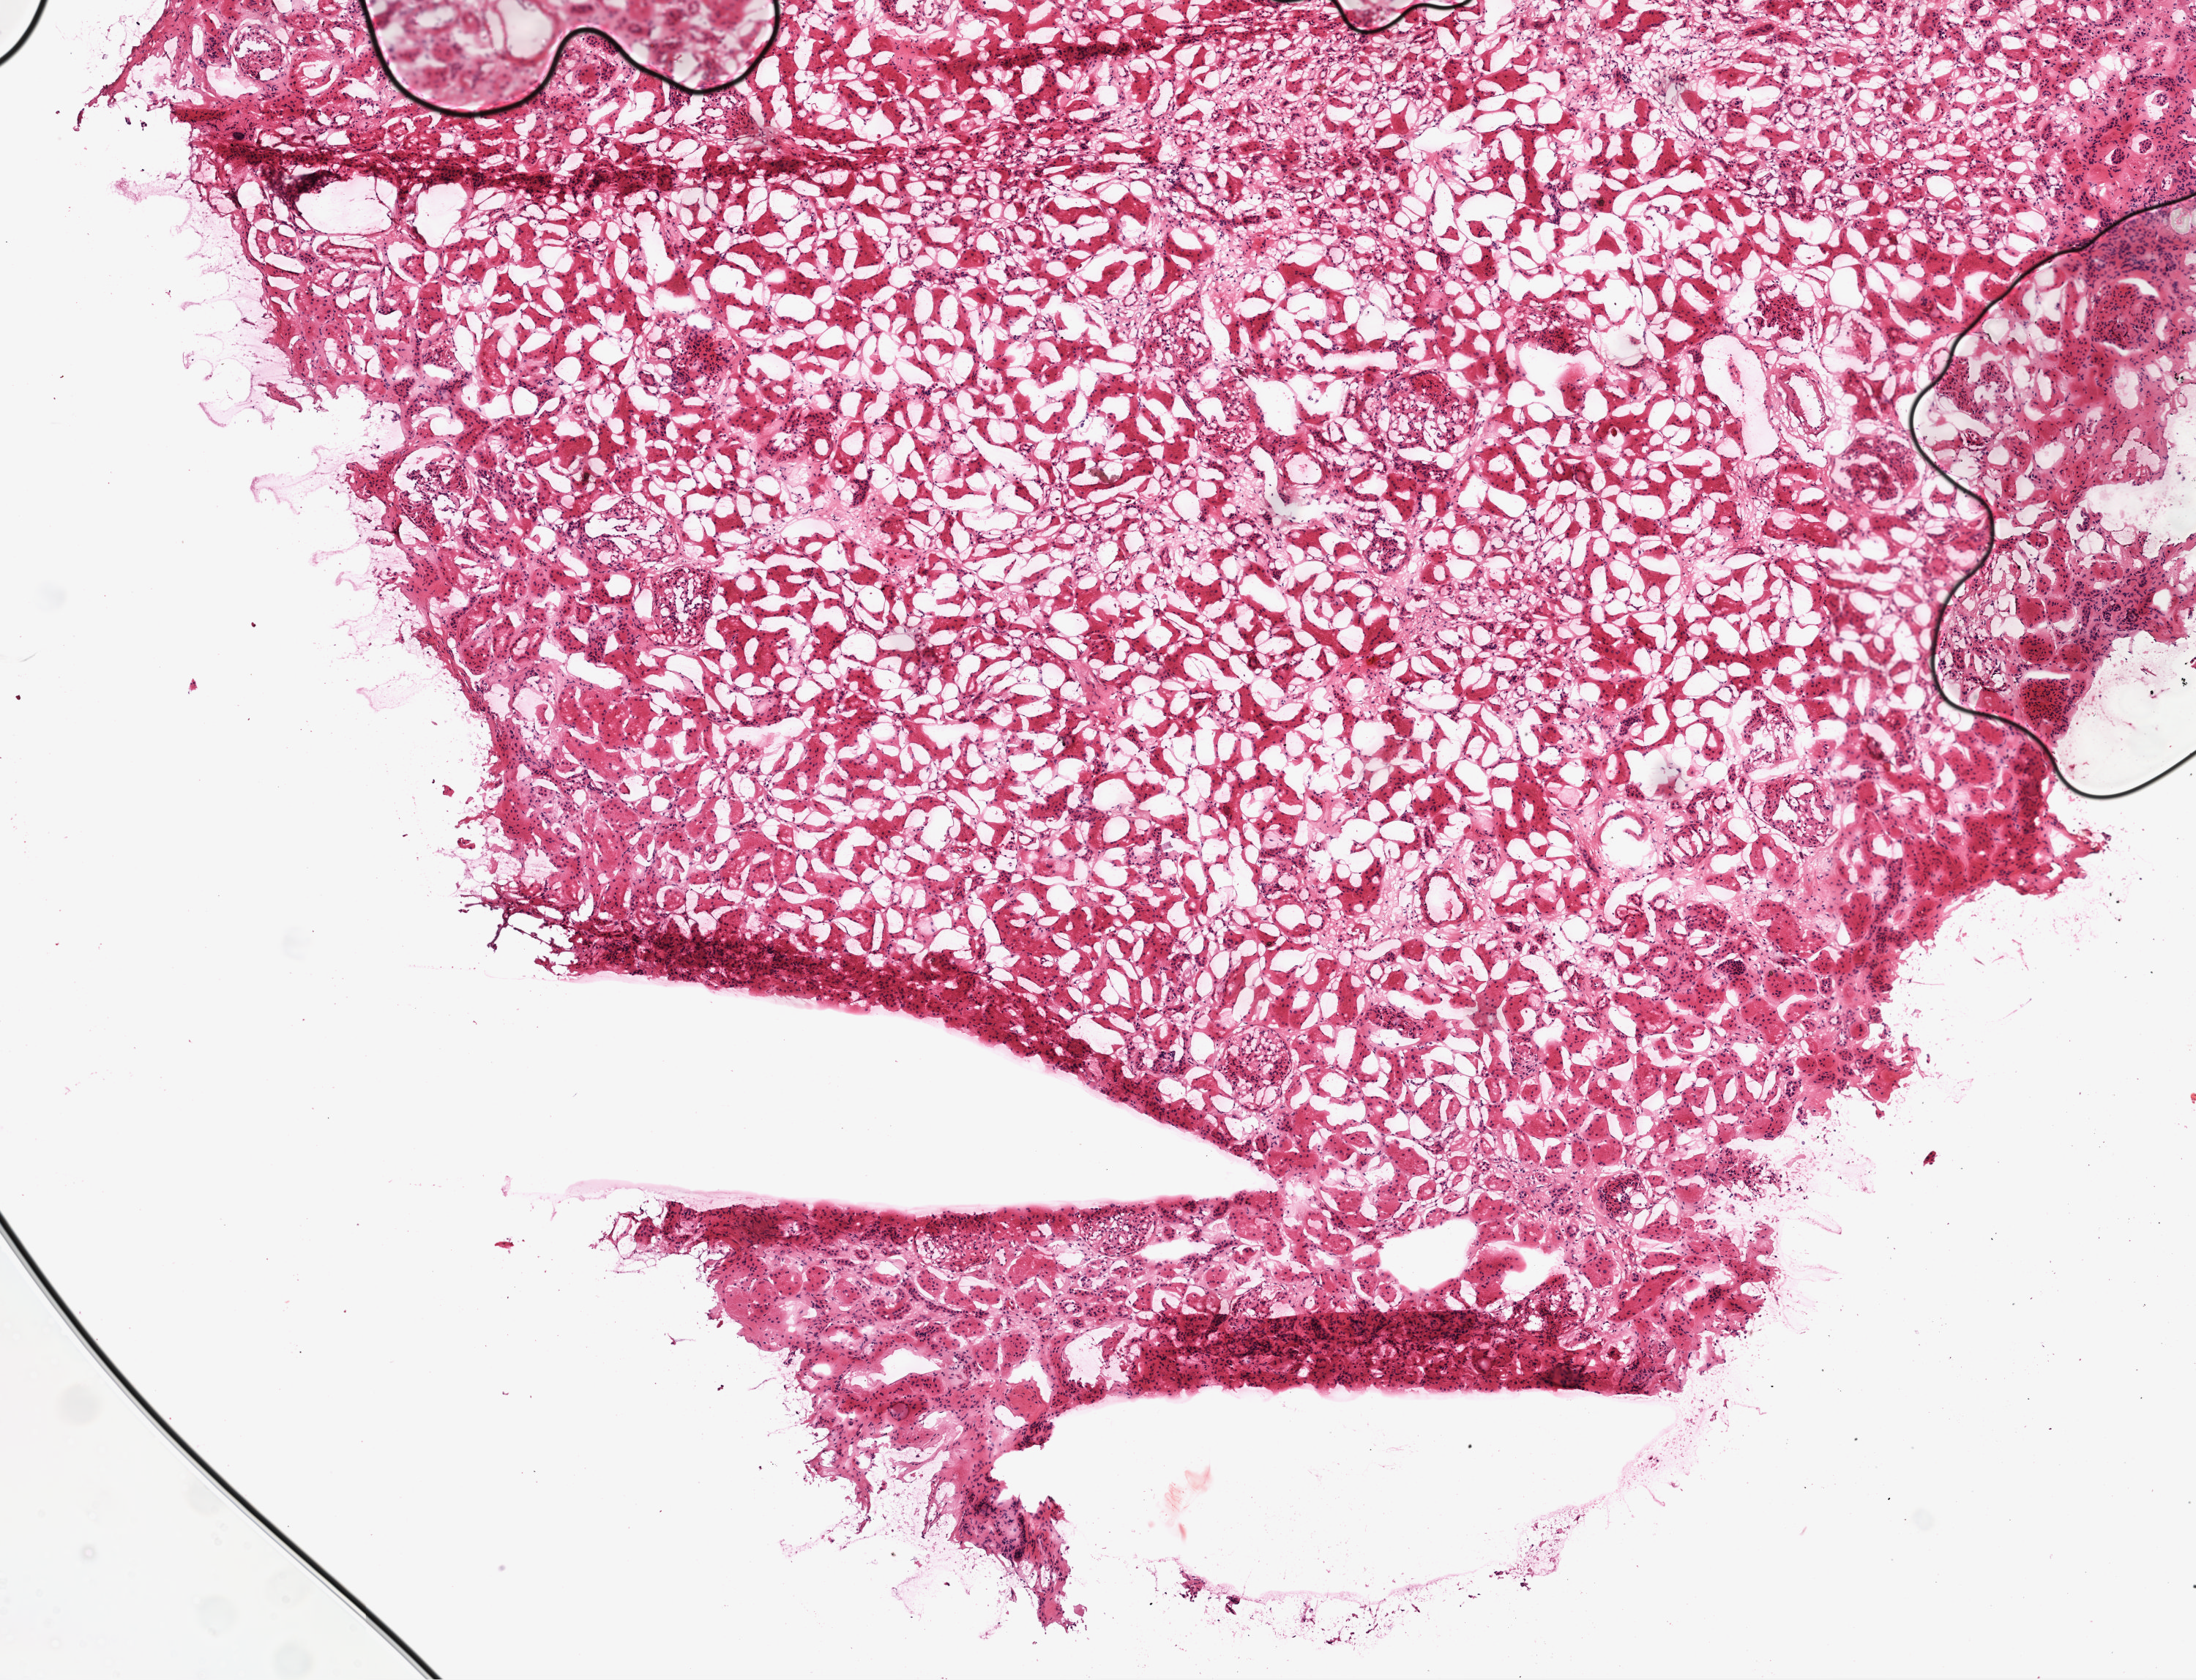
Whole-slide histology image, H&E, low-resolution overview of the scanned area, about 6.0 x 4.6 mm (acquisition: 20x scan), frozen section, kidney, solid tissue normal (non-tumour tissue) sample. Patient: male, age at initial diagnosis 56 years.
This section: solid tissue normal sample (biorepository sample class). Patient diagnosis: Clear cell adenocarcinoma, NOS.